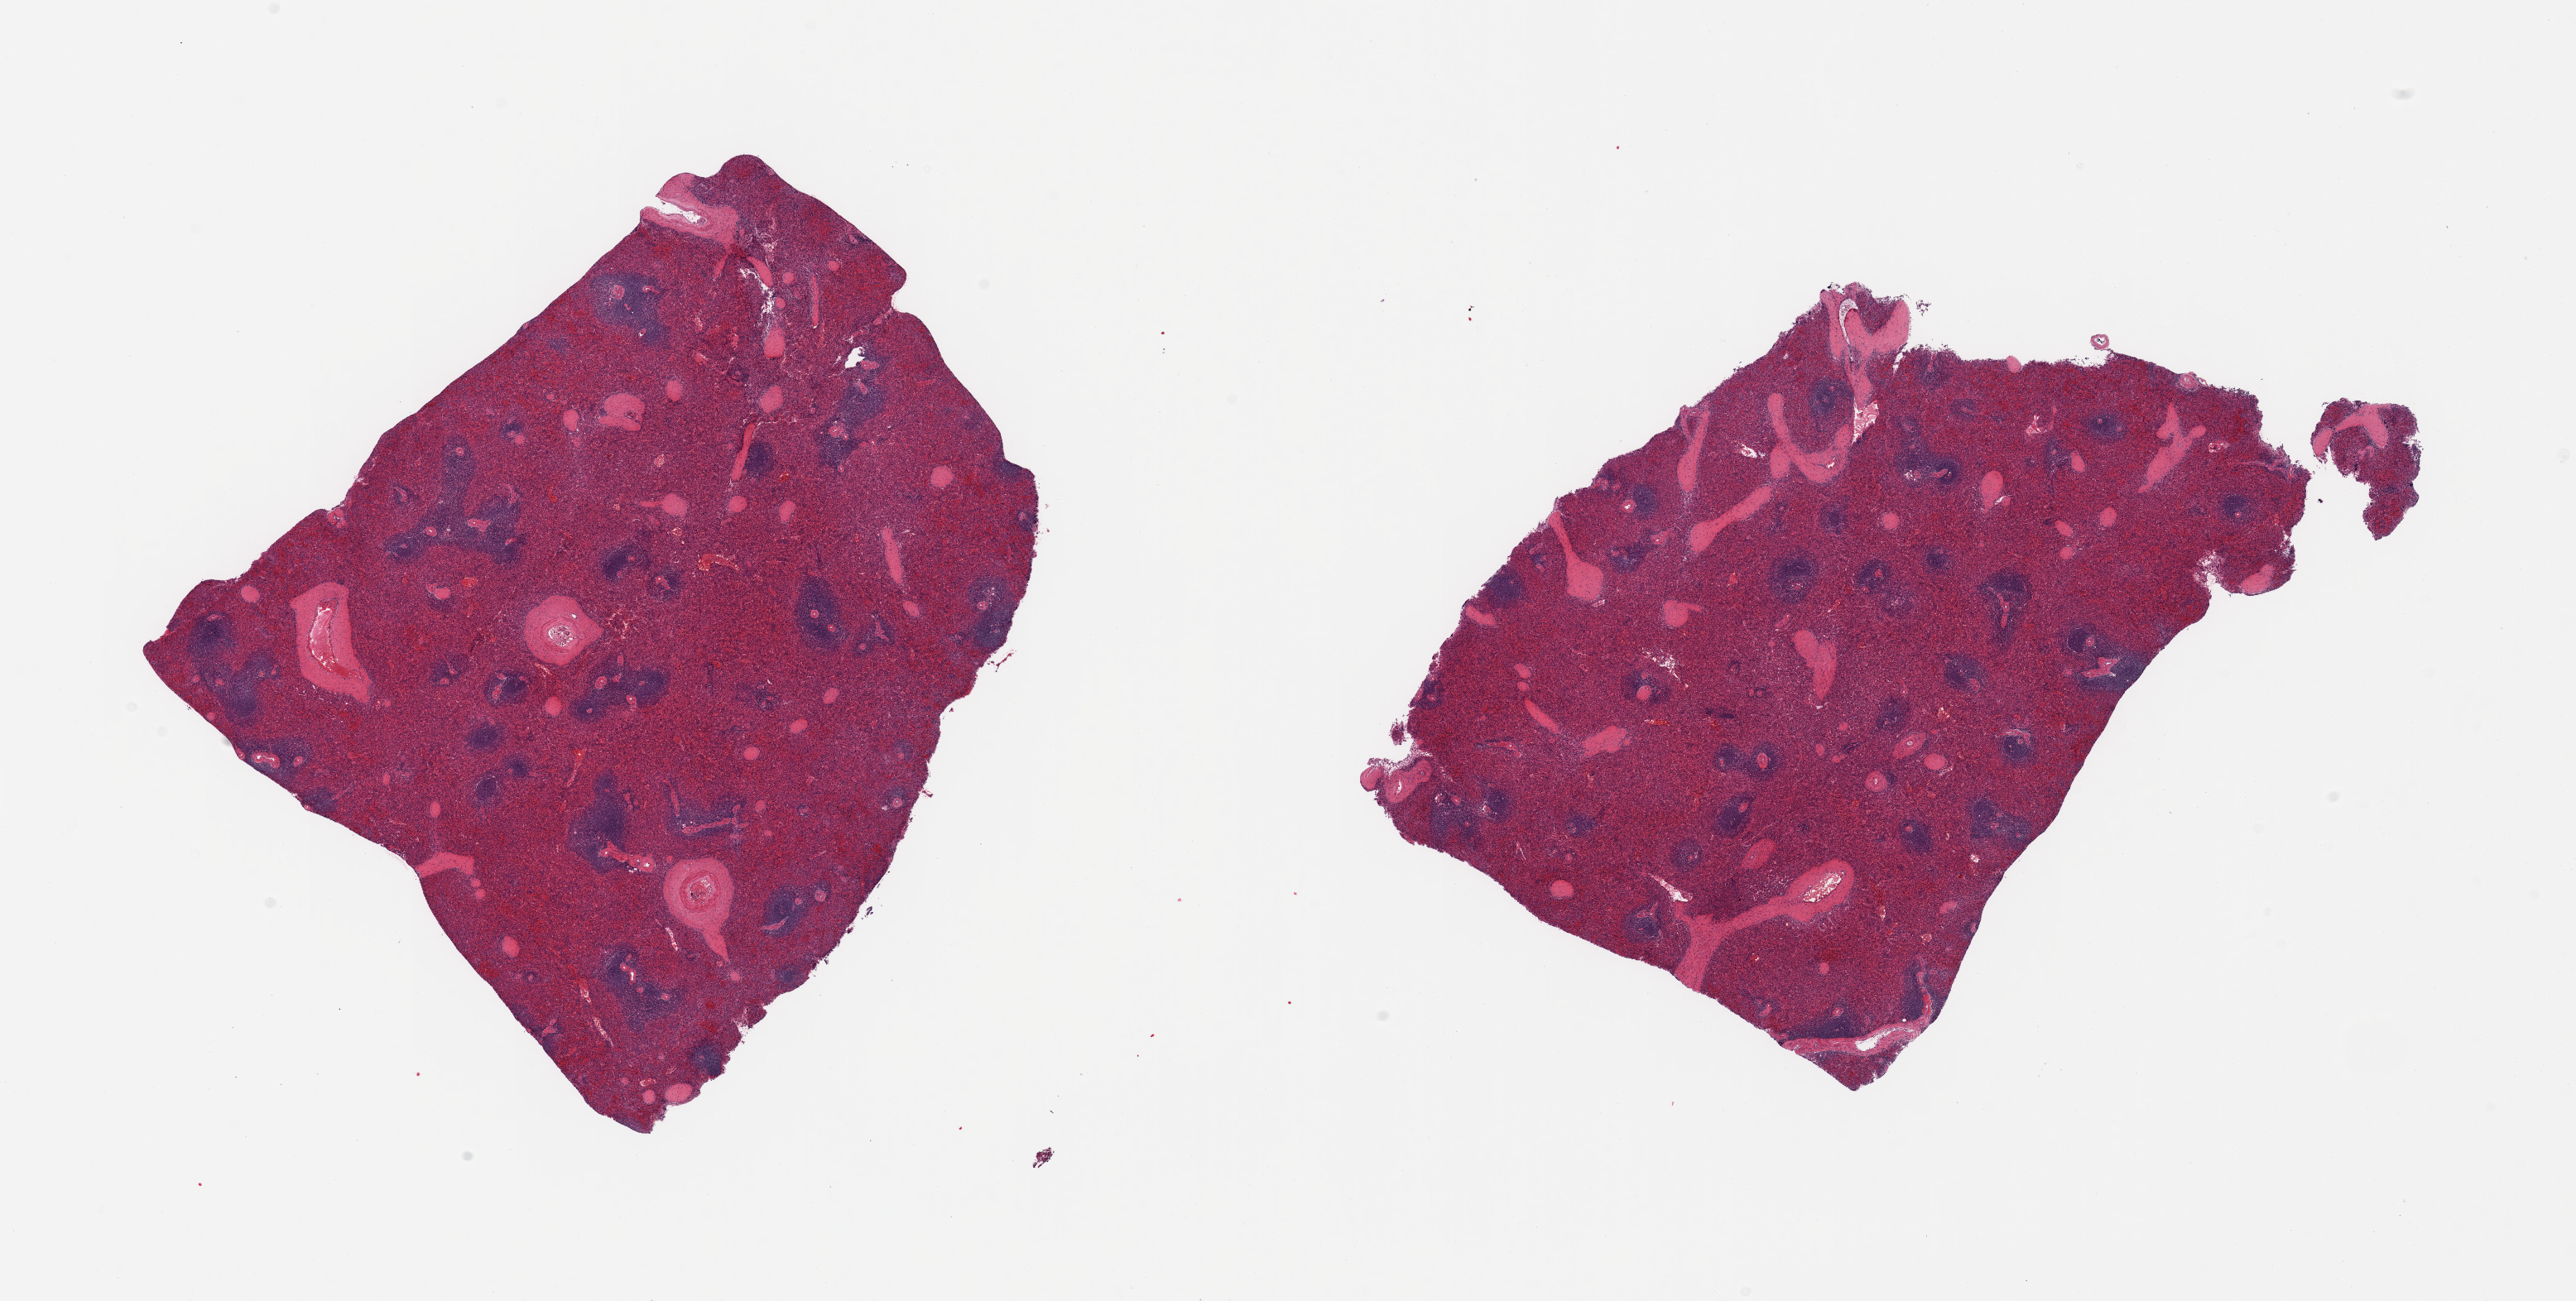
H&E whole-slide image, brightfield — whole scanned area (about 24.6 x 12.4 mm, slide scanned at 20x) shown as a low-resolution overview, PAXgene-fixed paraffin-embedded (PFPE) section, sampled site (target tissue): spleen, donor tissue sample. Donor sex: male.
Reviewer comment on this tissue sample: 2 pieces; congestion.